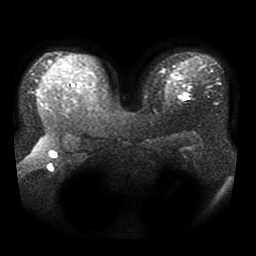
Breast MRI, one axial slice; slice 28 of 41 in the series (ordered by position); diffusion-weighted series; image 2 of 4 stored at this slice position (different b-values; order by instance number); 1.5 T; 5 mm slice thickness; 256 × 256 image matrix. Female patient.
Structures marked on this image (outlined manually by an expert reader):
- tumour on diffusion-weighted imaging: bounding box <185,94,188,99> (left, top, right, bottom; pixels)